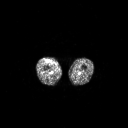
FDG PET of an extremity soft-tissue mass (from a PET/CT study), one axial slice. Position 225 of 311 along the scan axis. 3.27 mm slice thickness. 128 × 128 image matrix, field of view 700 × 700 mm. Male patient, age 56 years. From the clinical record (not read from this slice): histological type: pleiomorphic leiomyosarcoma; grade: intermediate; site of the primary tumour: right thigh.
Annotated regions visible in this slice (expert contour drawn on MRI and transferred to this co-registered scan by the dataset authors):
- gross tumour volume including surrounding oedema: bounding box [x1, y1, x2, y2] px = [47, 60, 51, 63]